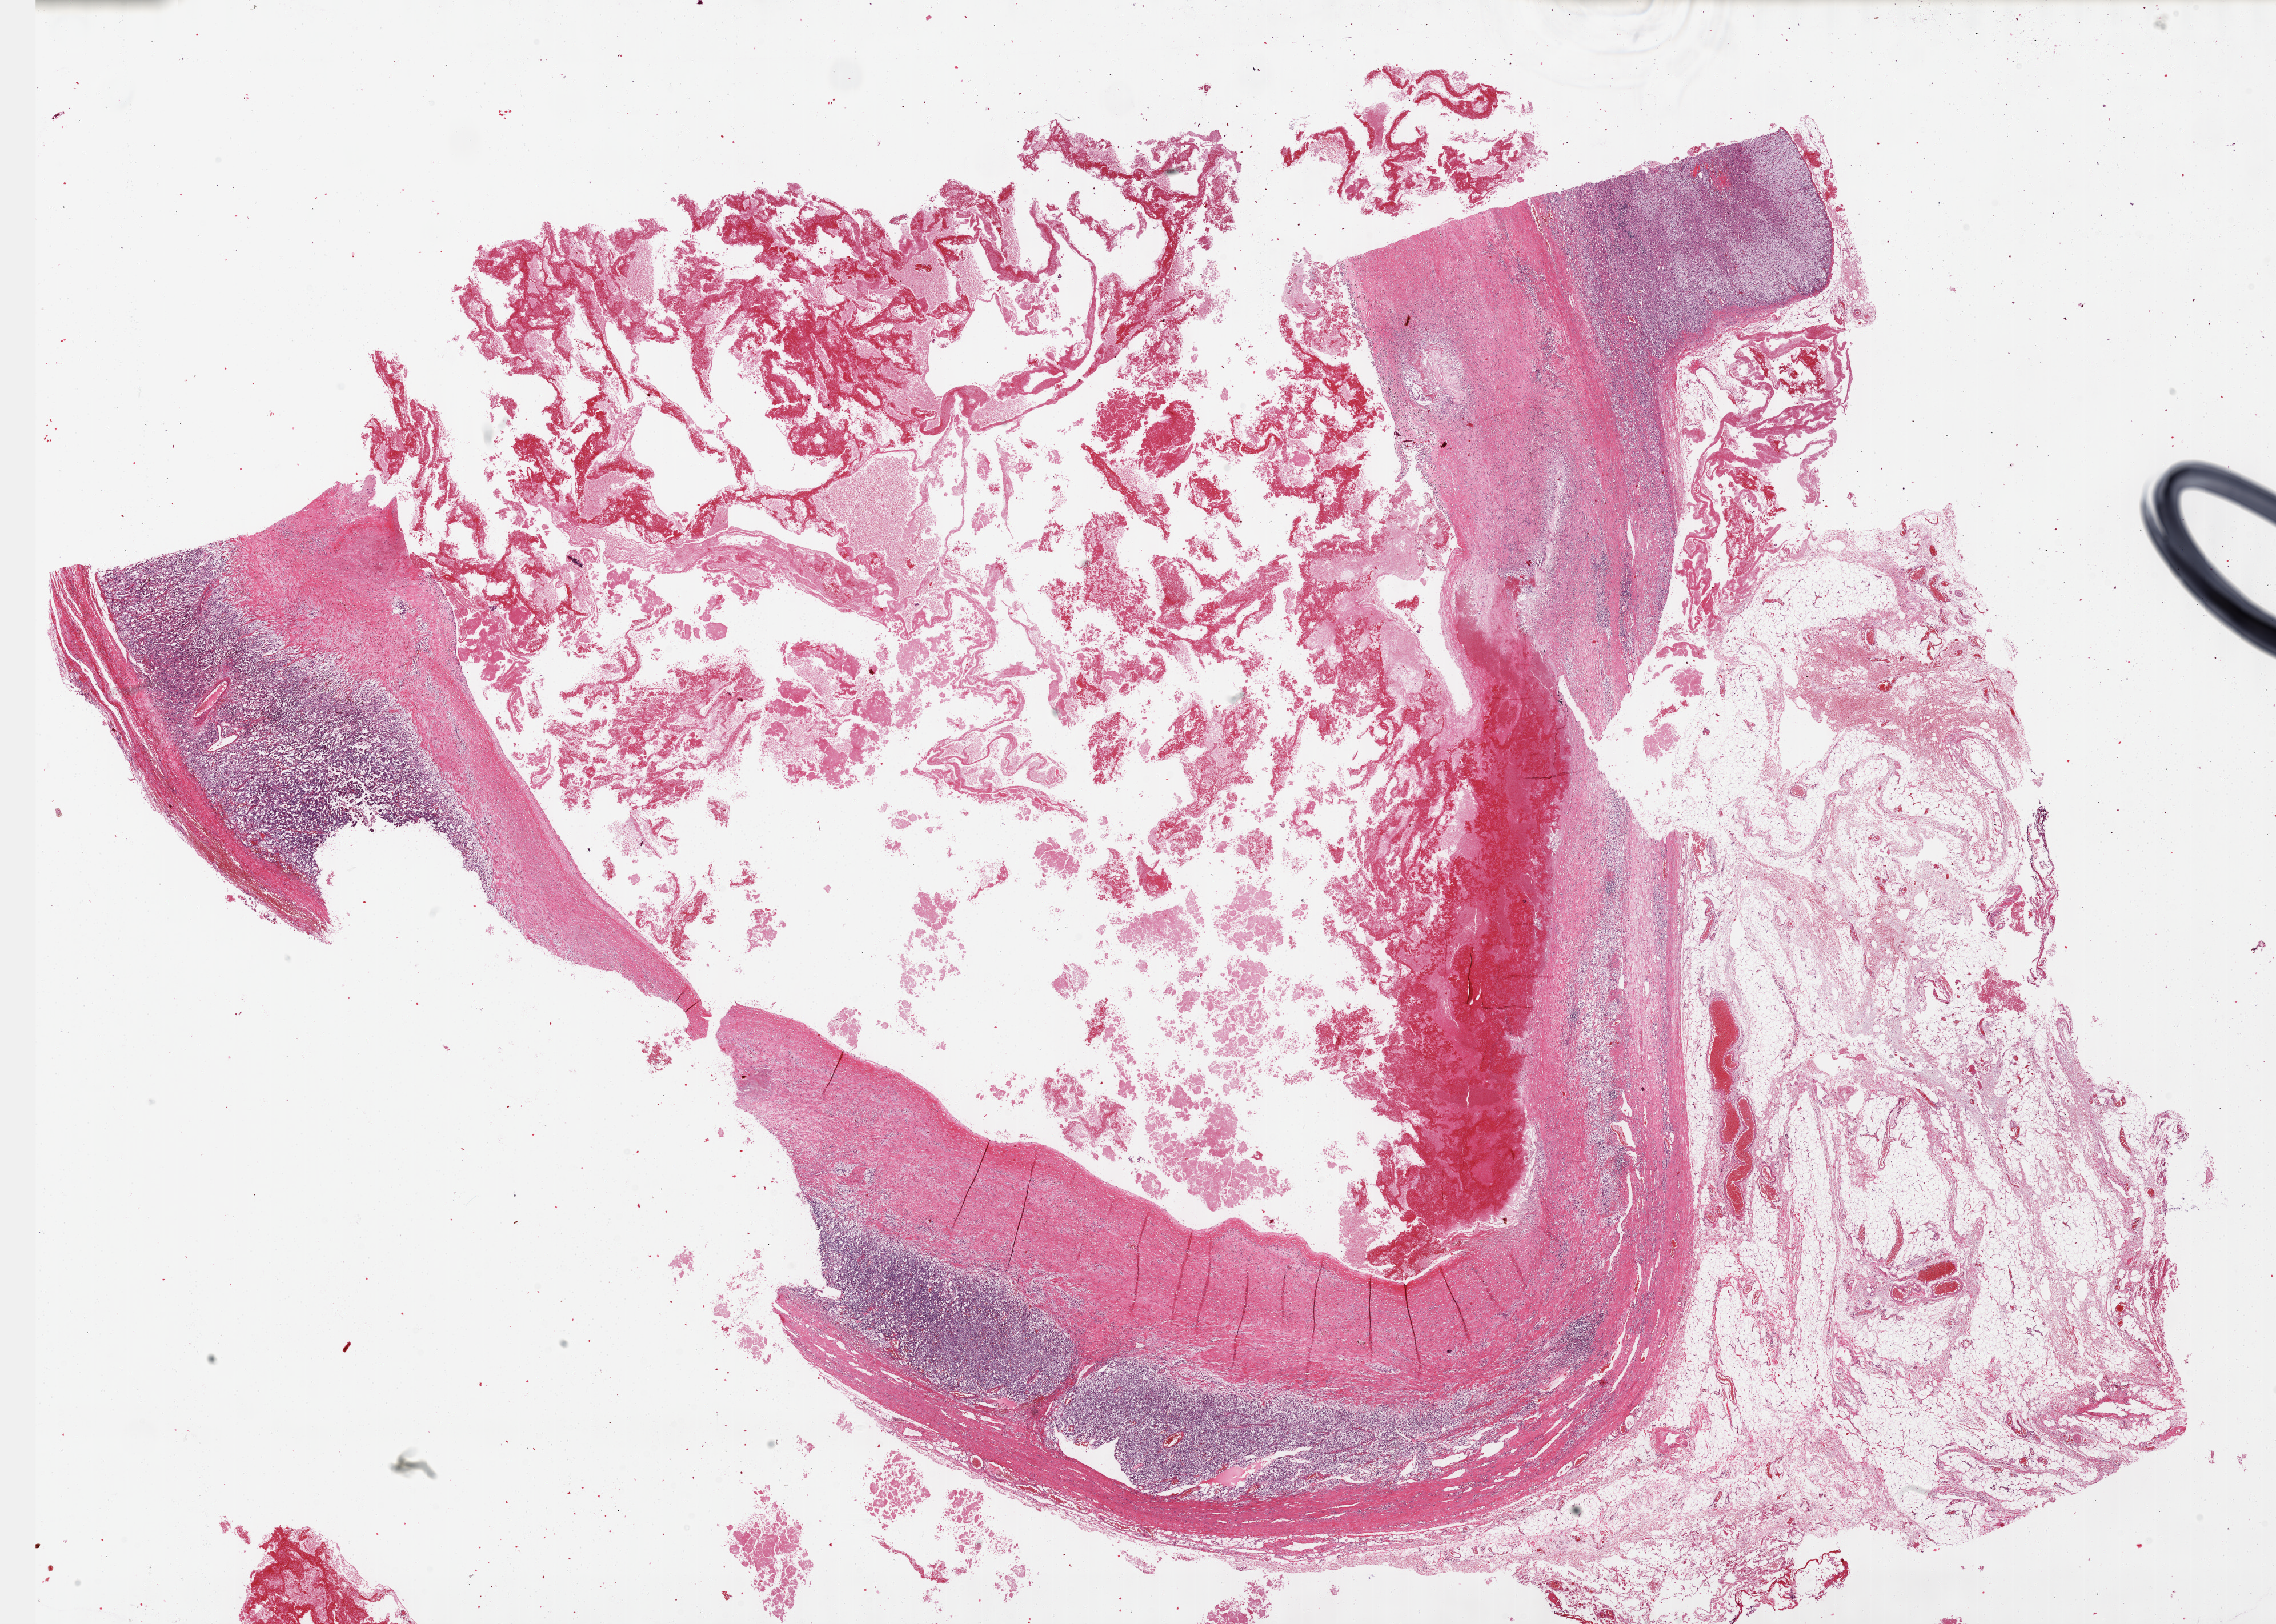
Digitized H&E-stained tissue section (whole slide) — shown as a low-resolution overview of the whole scanned area (about 32.2 x 23.0 mm, from a 40x scan), FFPE section, sample: primary tumour, adrenal gland. Patient: male, age at initial diagnosis 57 years.
Diagnosis: Pheochromocytoma, NOS.